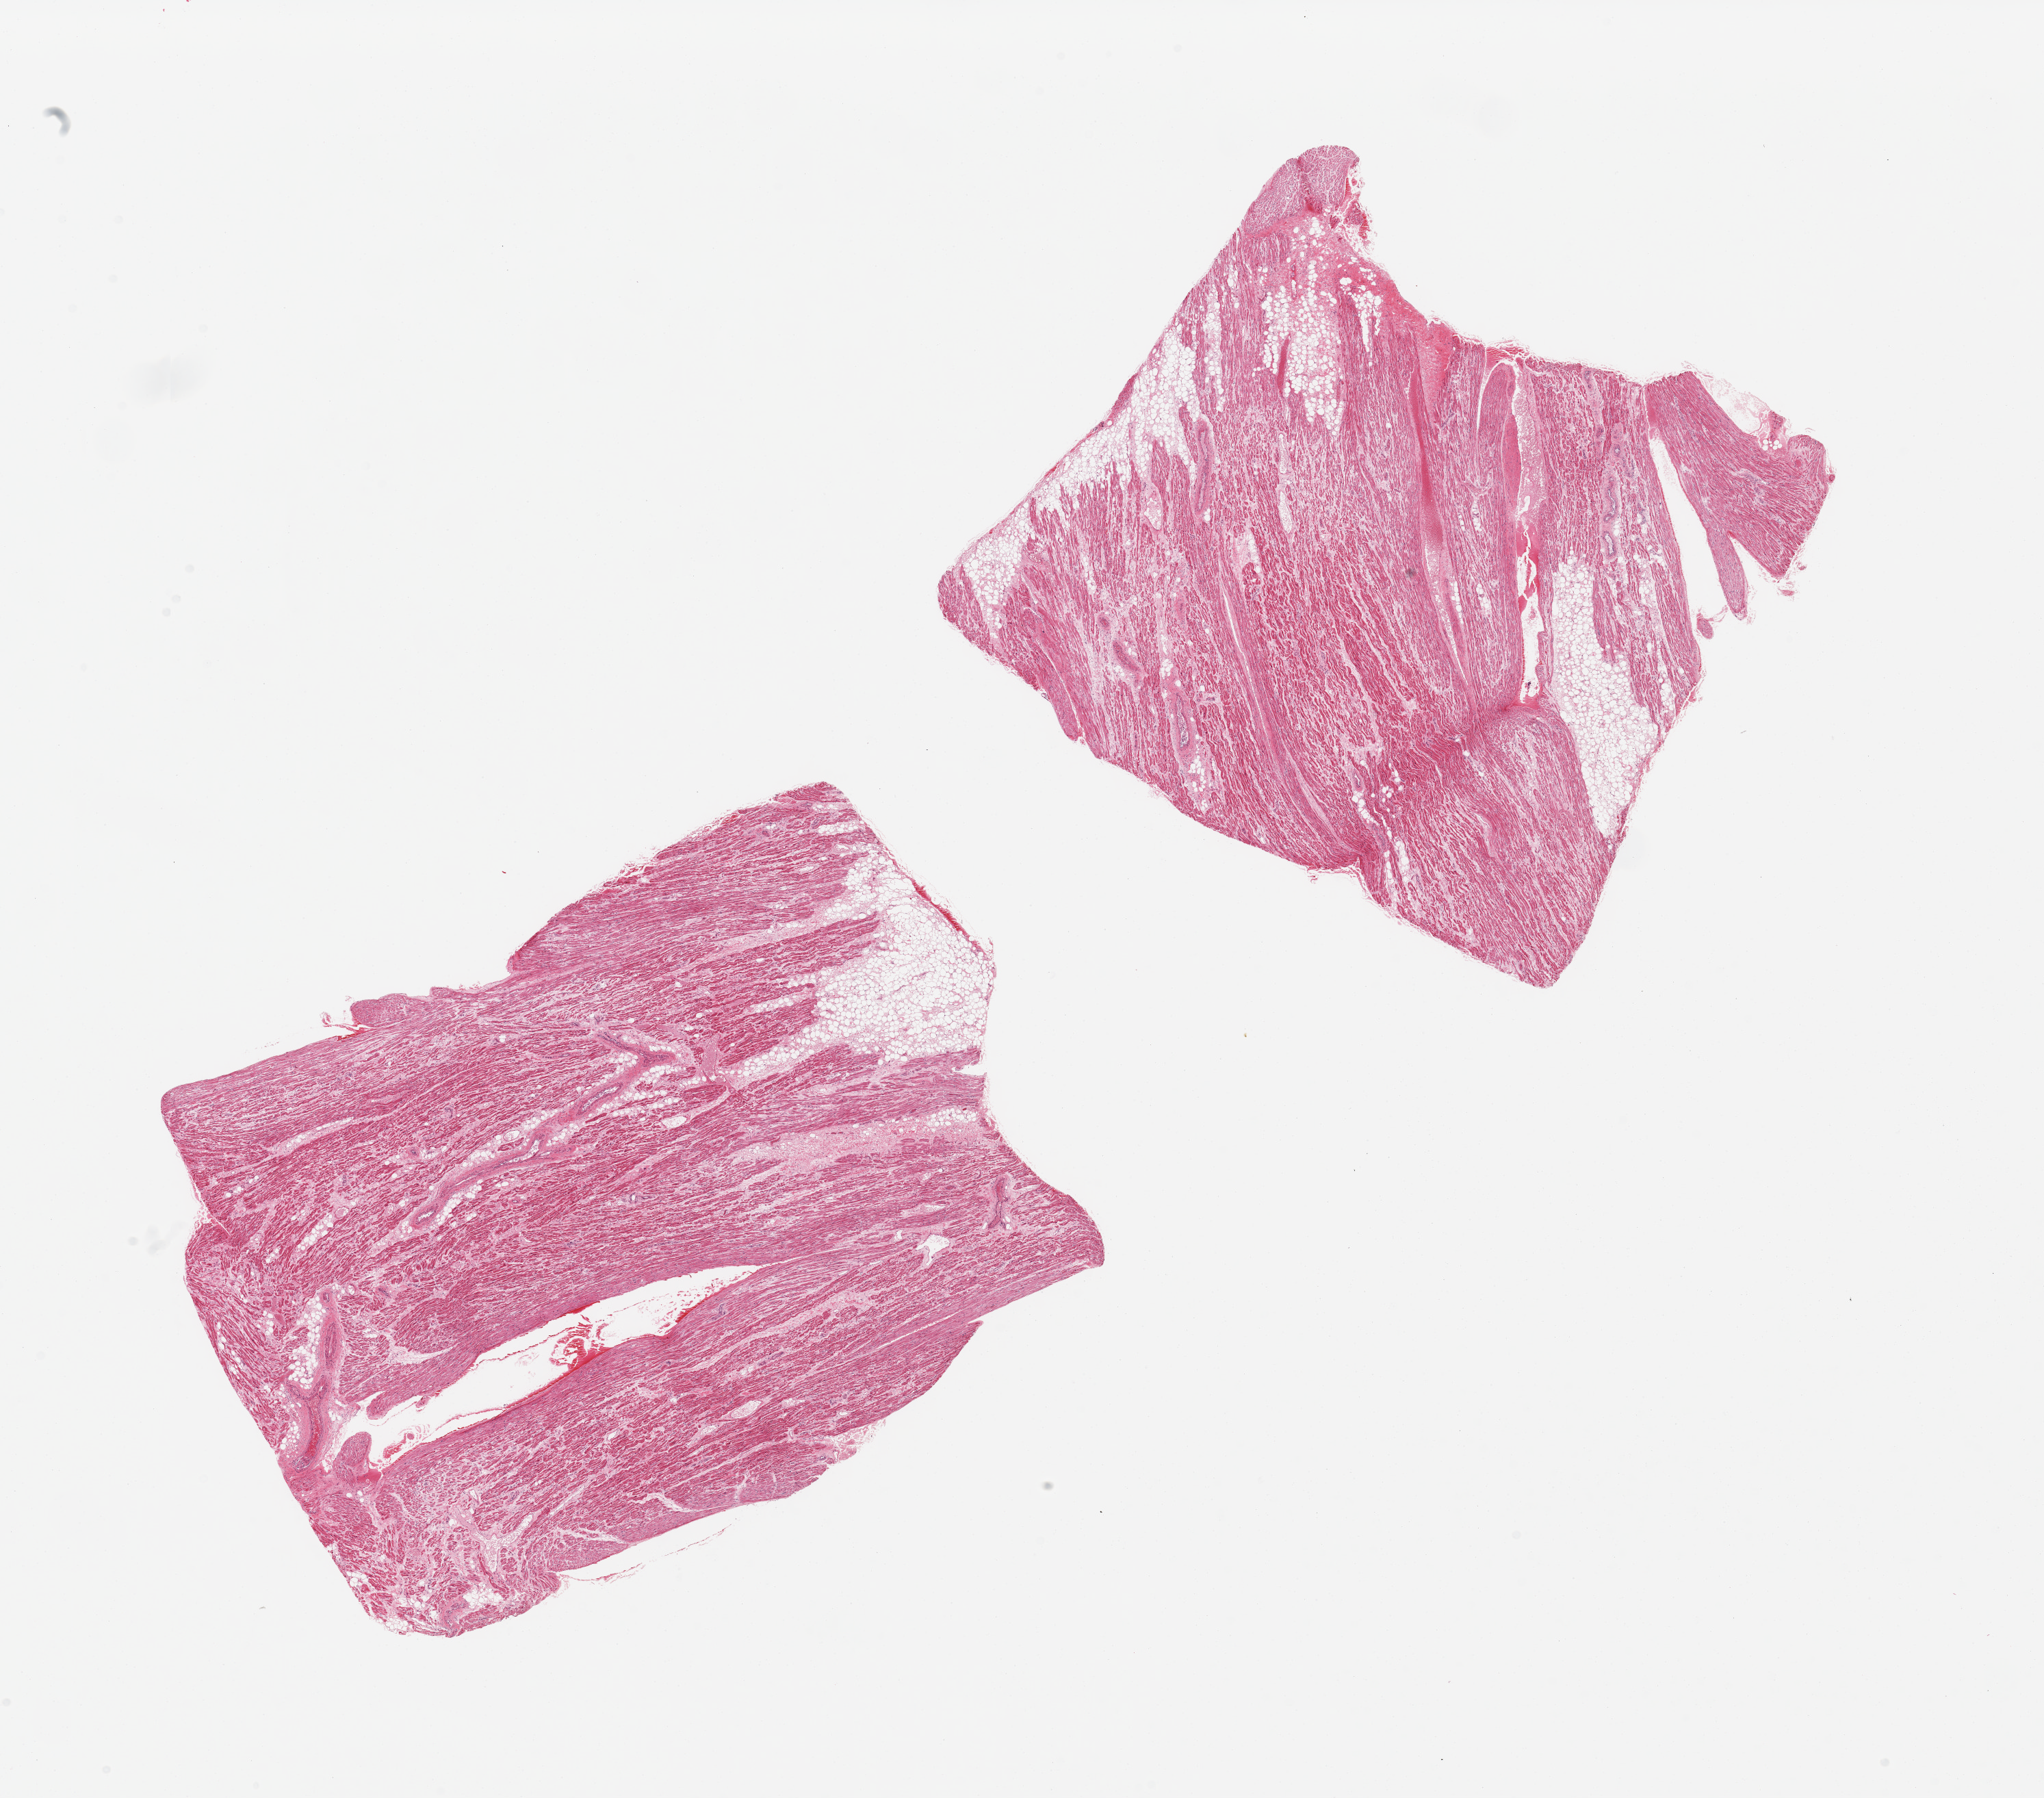
H&E whole-slide image, brightfield — low-resolution overview of the scanned area, about 23.6 x 20.8 mm (acquisition: 20x scan); PAXgene-fixed, paraffin-embedded tissue; target tissue: auricular appendage; donor tissue sample. Male donor.
Reviewer comment on this tissue sample: 2 pieces, no abnormalities.